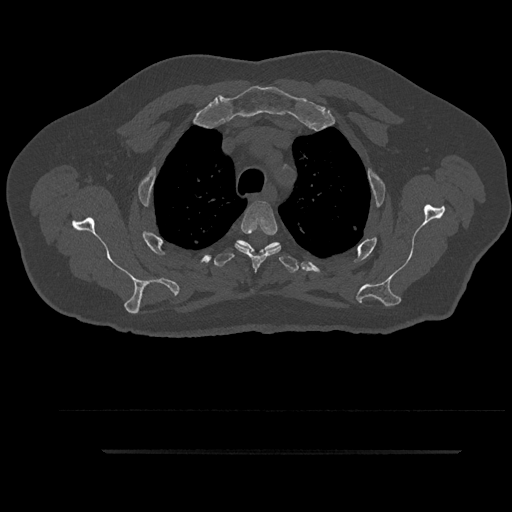
CT including the spine, one axial slice; slice 704 of 797 in the series (ordered by position); reconstruction kernel Br40s/3; 120 kVp; bone window (W 1800 / L 400 HU); 0.5 mm slice thickness; 512 × 512 image matrix, field of view 432 × 432 mm. Patient: male, 63 years. From the clinical record (not read from this slice): primary cancer: renal.
Outlined on this slice (semi-automatic segmentation, software-assisted and operator-edited):
- T3 vertebra: bounding box [x1, y1, x2, y2] px = [235, 200, 281, 270]
- T4 vertebra: [213, 240, 299, 273]